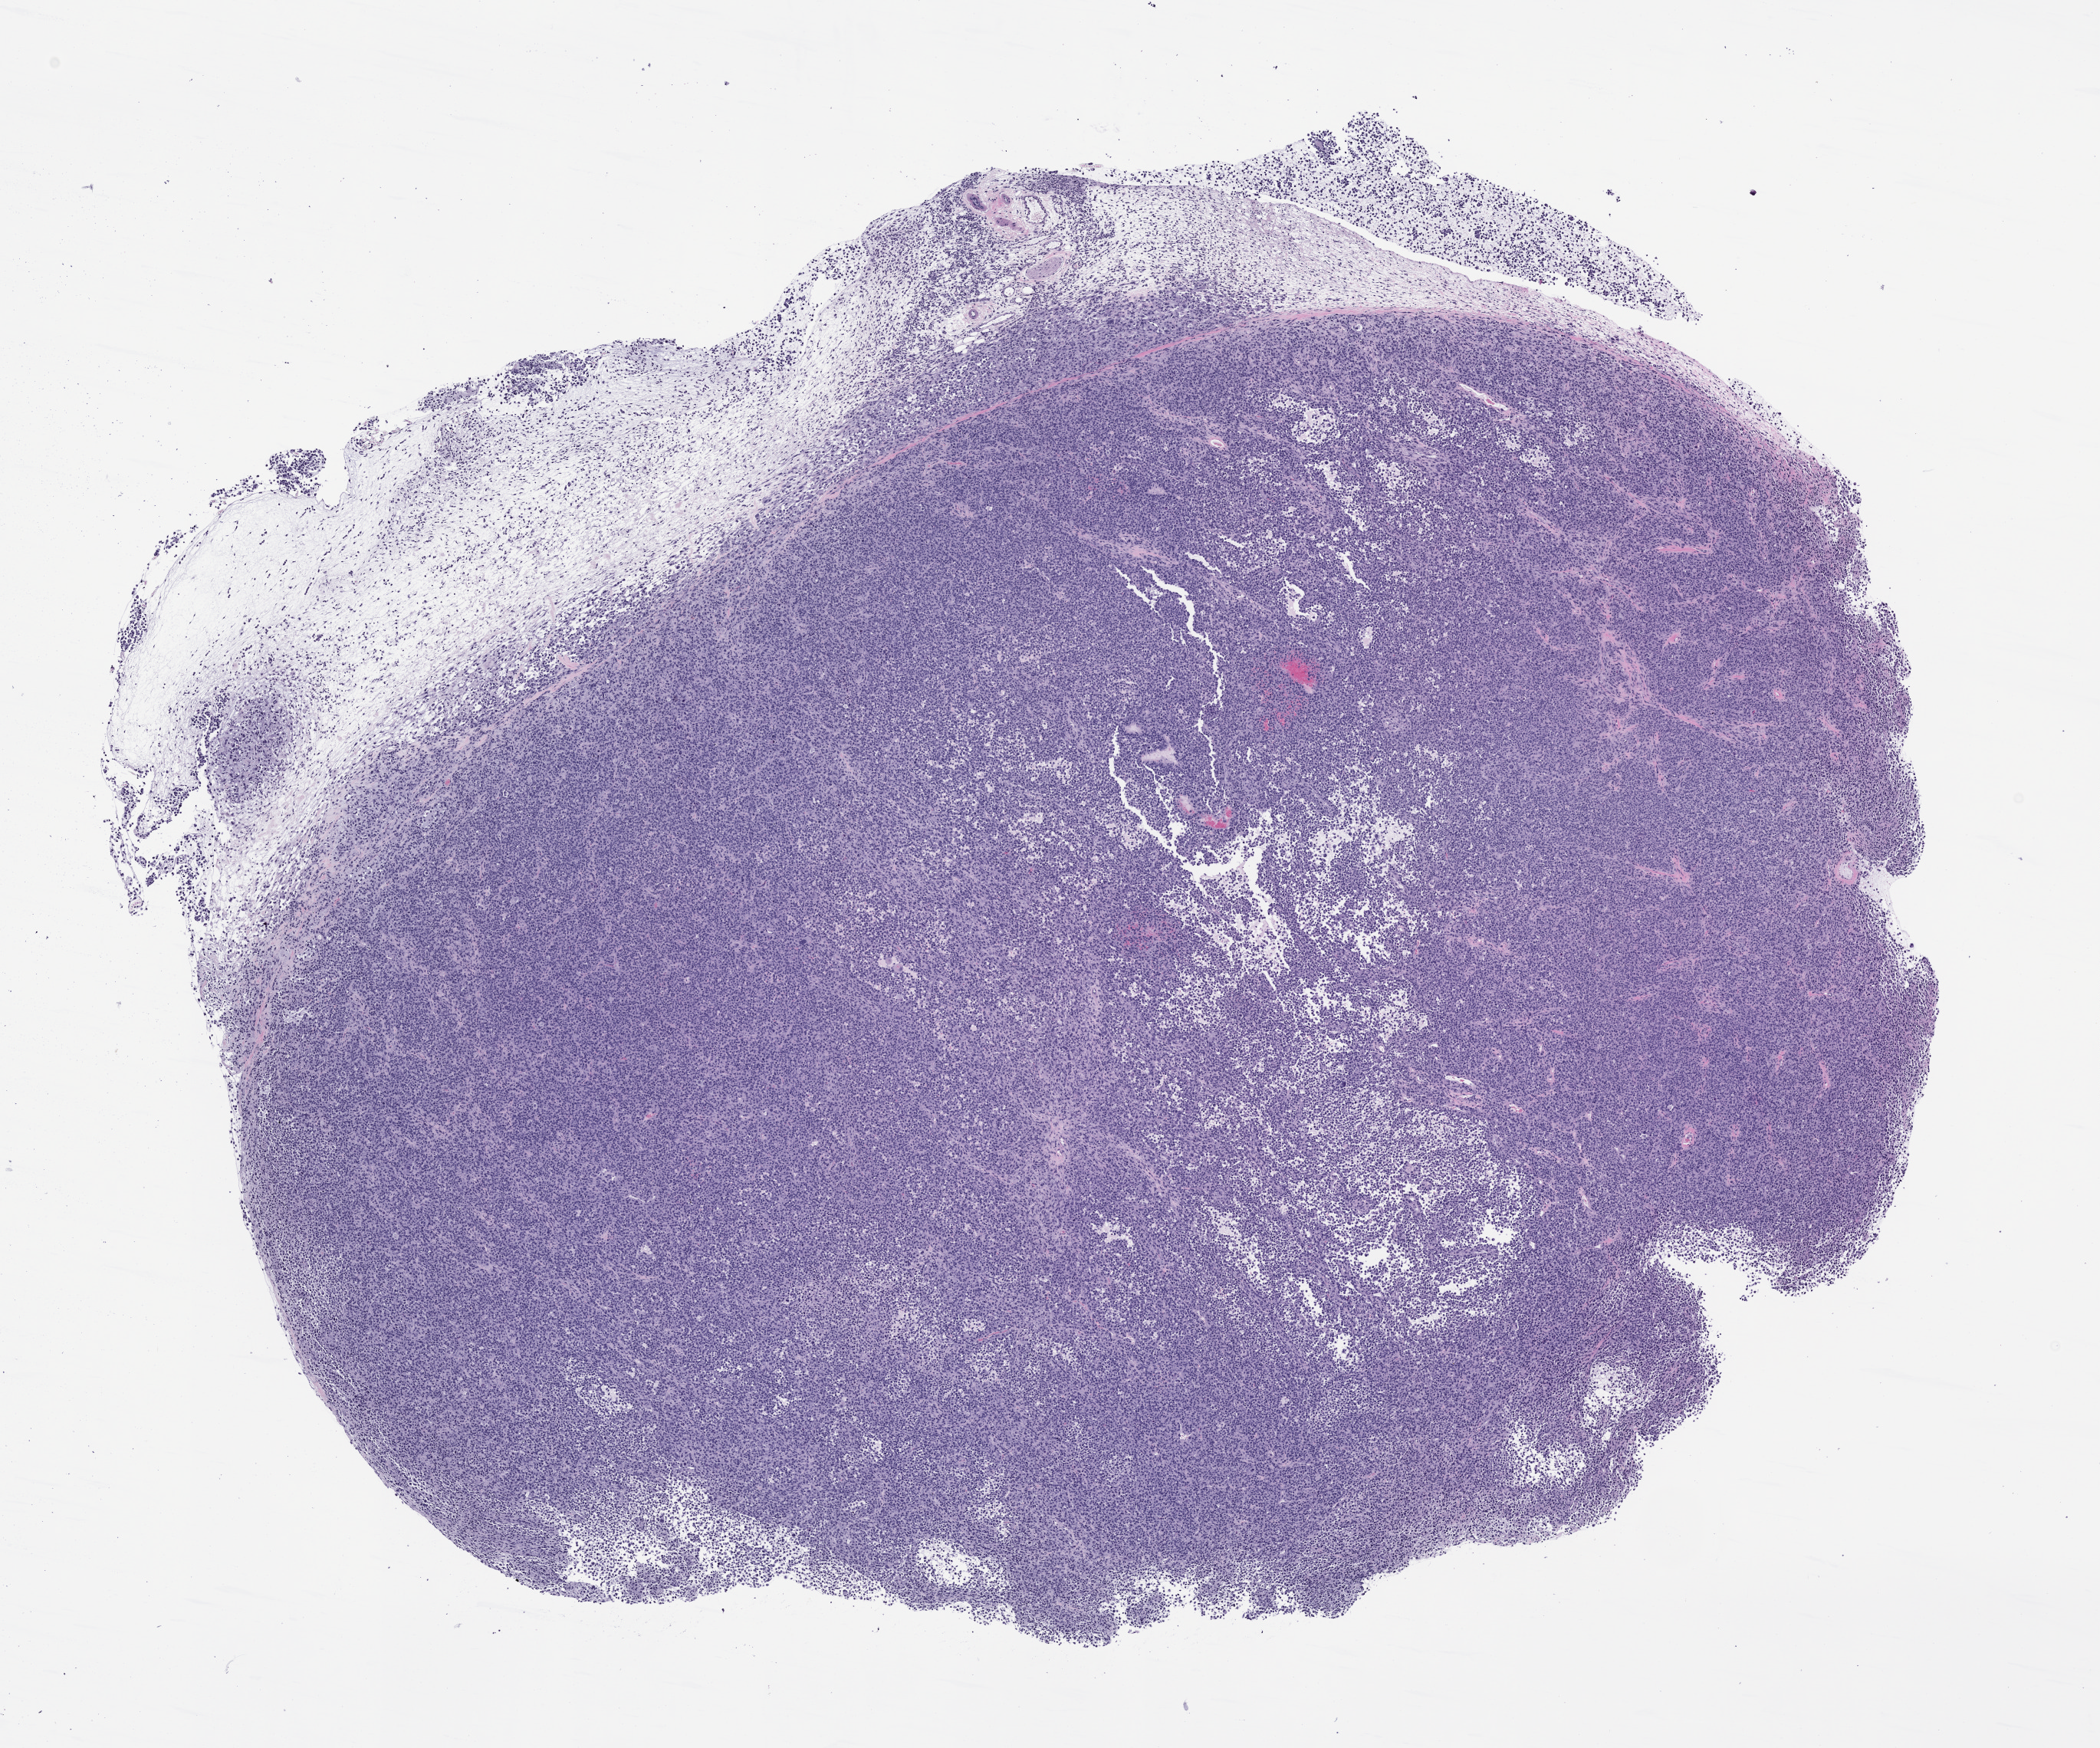
Hematoxylin and eosin (H&E) whole-slide image of a patient-derived xenograft (PDX) tumor grown in a mouse, passage 1 — a low-resolution overview of the entire scanned area, about 11.0 x 9.2 mm; formalin-fixed paraffin-embedded section; originating tumor site category: musculoskeletal.
Originating patient diagnosis: Rhabdomyosarcoma.